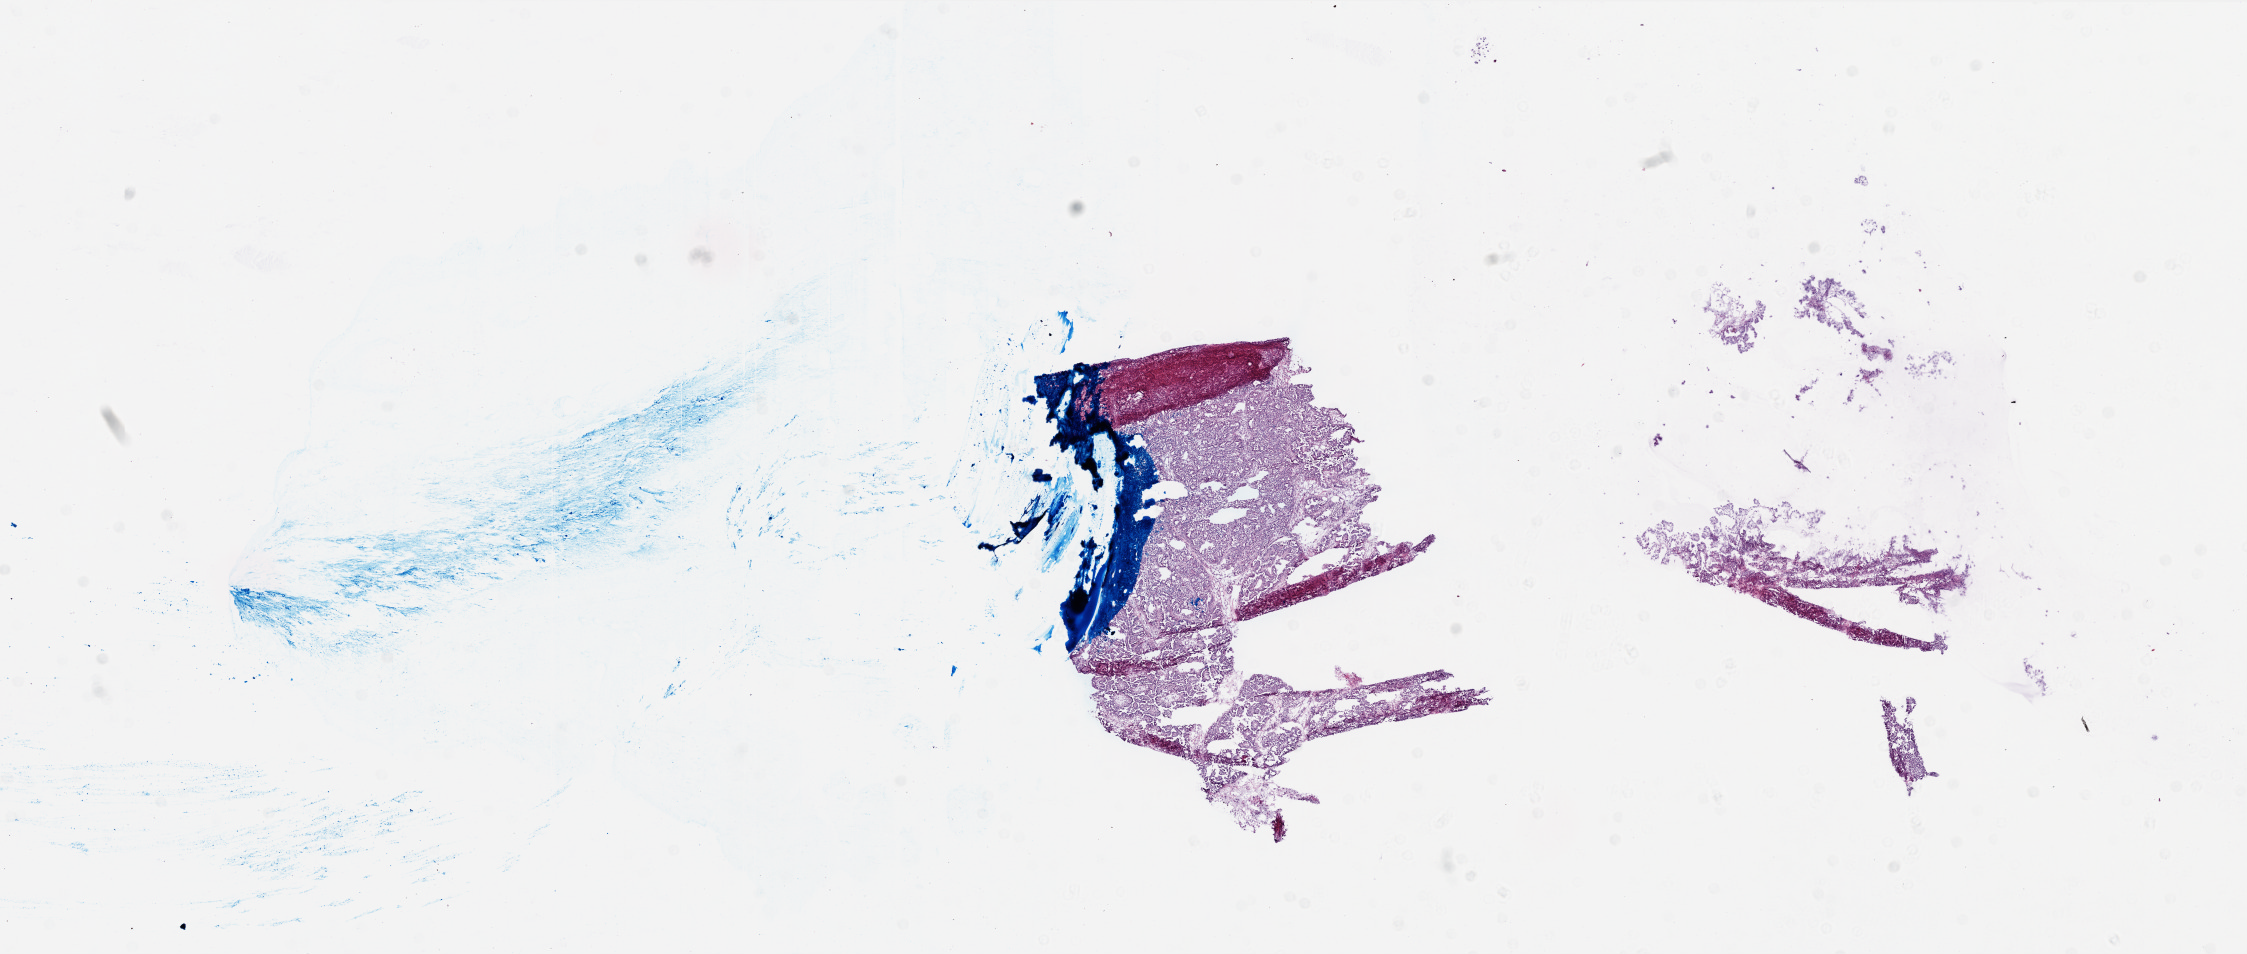
H&E whole-slide image — whole scanned area (about 18.0 x 7.6 mm, slide scanned at 20x) shown as a low-resolution overview; frozen section from the top of the tissue portion; sample: primary tumour, ovary. Female patient; age at initial diagnosis 55 years. Histologic grade: G3 (poorly differentiated). Pathologist review of this section (percent, as recorded): tumour cells 100%, tumour nuclei 98%, normal cells 0%, stromal cells 0%, necrosis 0%.
FIGO stage: IIIC. Histologic diagnosis: Serous cystadenocarcinoma, NOS (specified parts of peritoneum).